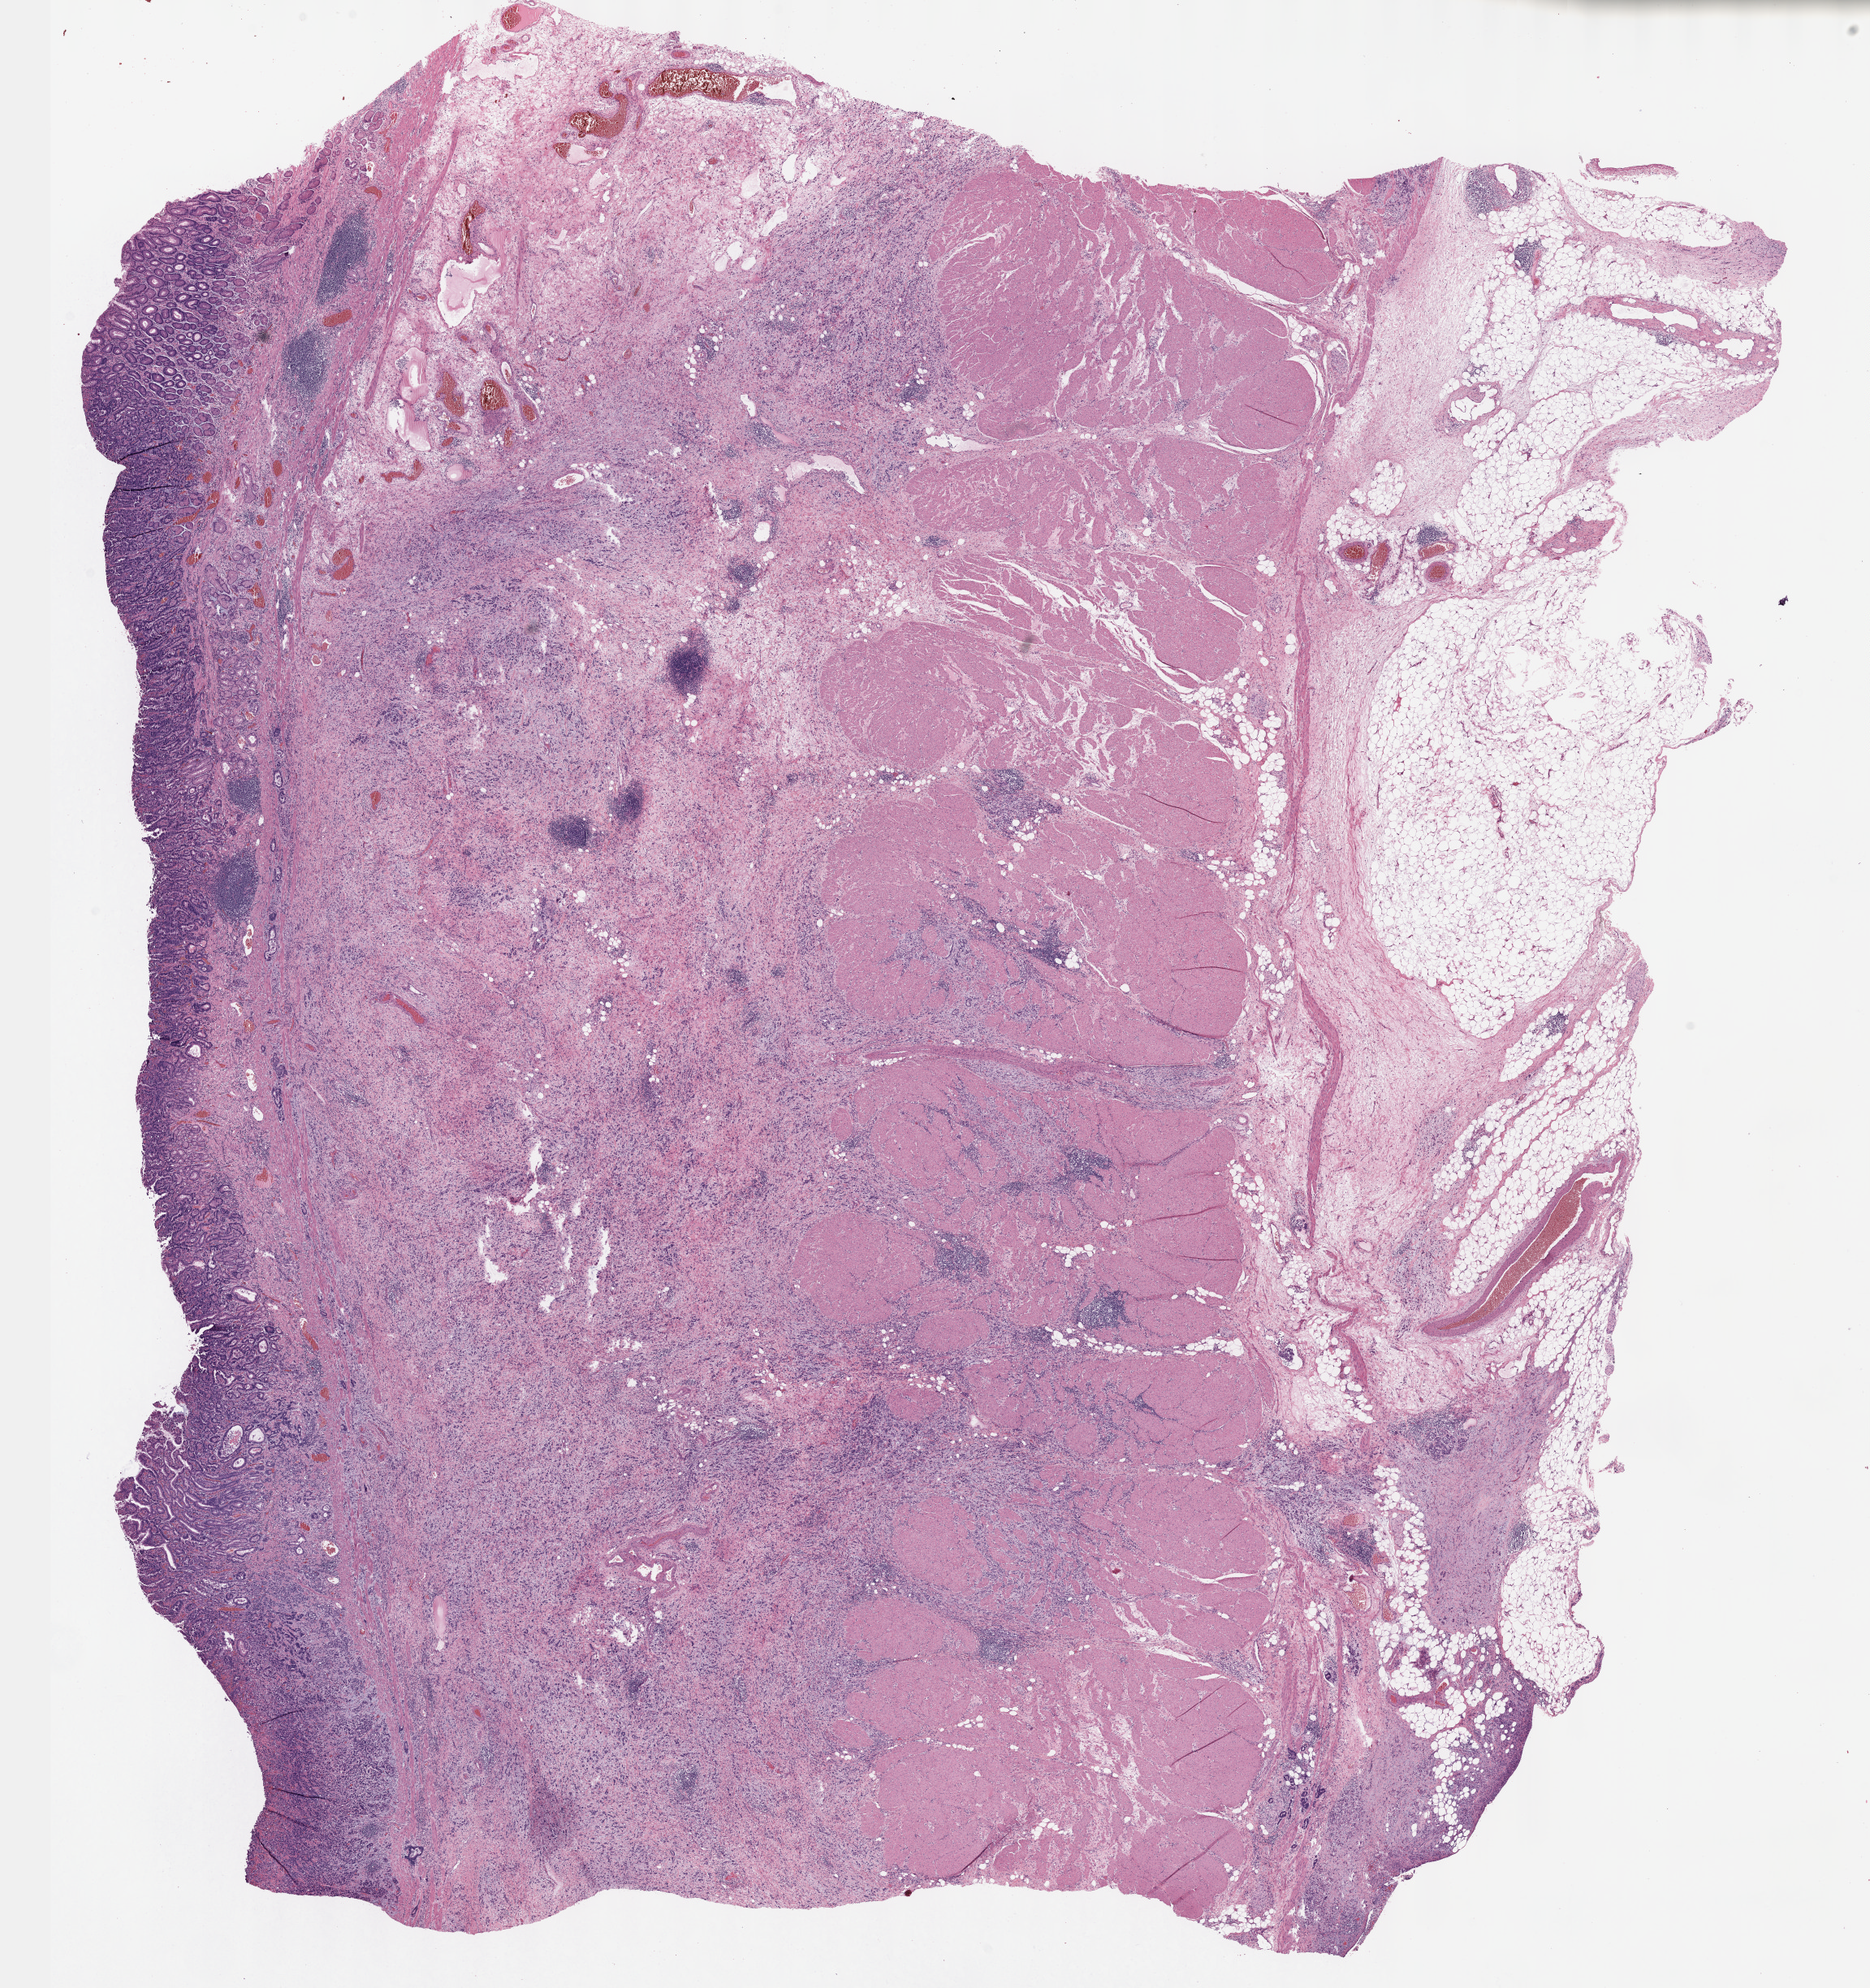
Whole-slide histology image, H&E, shown as a low-resolution overview of the whole scanned area (about 18.6 x 19.8 mm), FFPE section, sample: primary tumour, stomach. Male, age 43 years at initial diagnosis. Histologic grade: G3 (poorly differentiated).
• lymph nodes positive (case pathology): 9 of 53 examined
• AJCC pathologic stage: IIIB (7th edition)
• pathologic diagnosis: Adenocarcinoma, intestinal type (body of stomach)